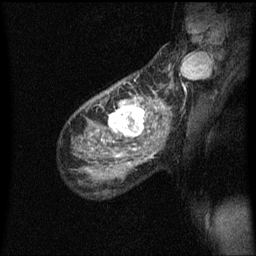
Breast MRI (dynamic contrast-enhanced), one sagittal slice; slice 40 of 60 in the series (ordered by position); dynamic contrast-enhanced series, image 2 of 3 at this slice position (ordered by acquisition); 1.5 T; TE 4.2 ms, TR 8.4 ms; 2 mm slice thickness; 256 × 256 image matrix. Female patient, age 49 years.
Structures marked on this image (semi-automatic segmentation, software-assisted and operator-edited):
- analysis volume of interest (the breast-tissue region the enhancement analysis was run in; not a lesion): box from (x=103, y=90) to (x=157, y=151) px
- tumour enhancement mask (voxels above the 70 % enhancement threshold inside the analysis volume of interest): (x=109, y=92)–(x=157, y=151)